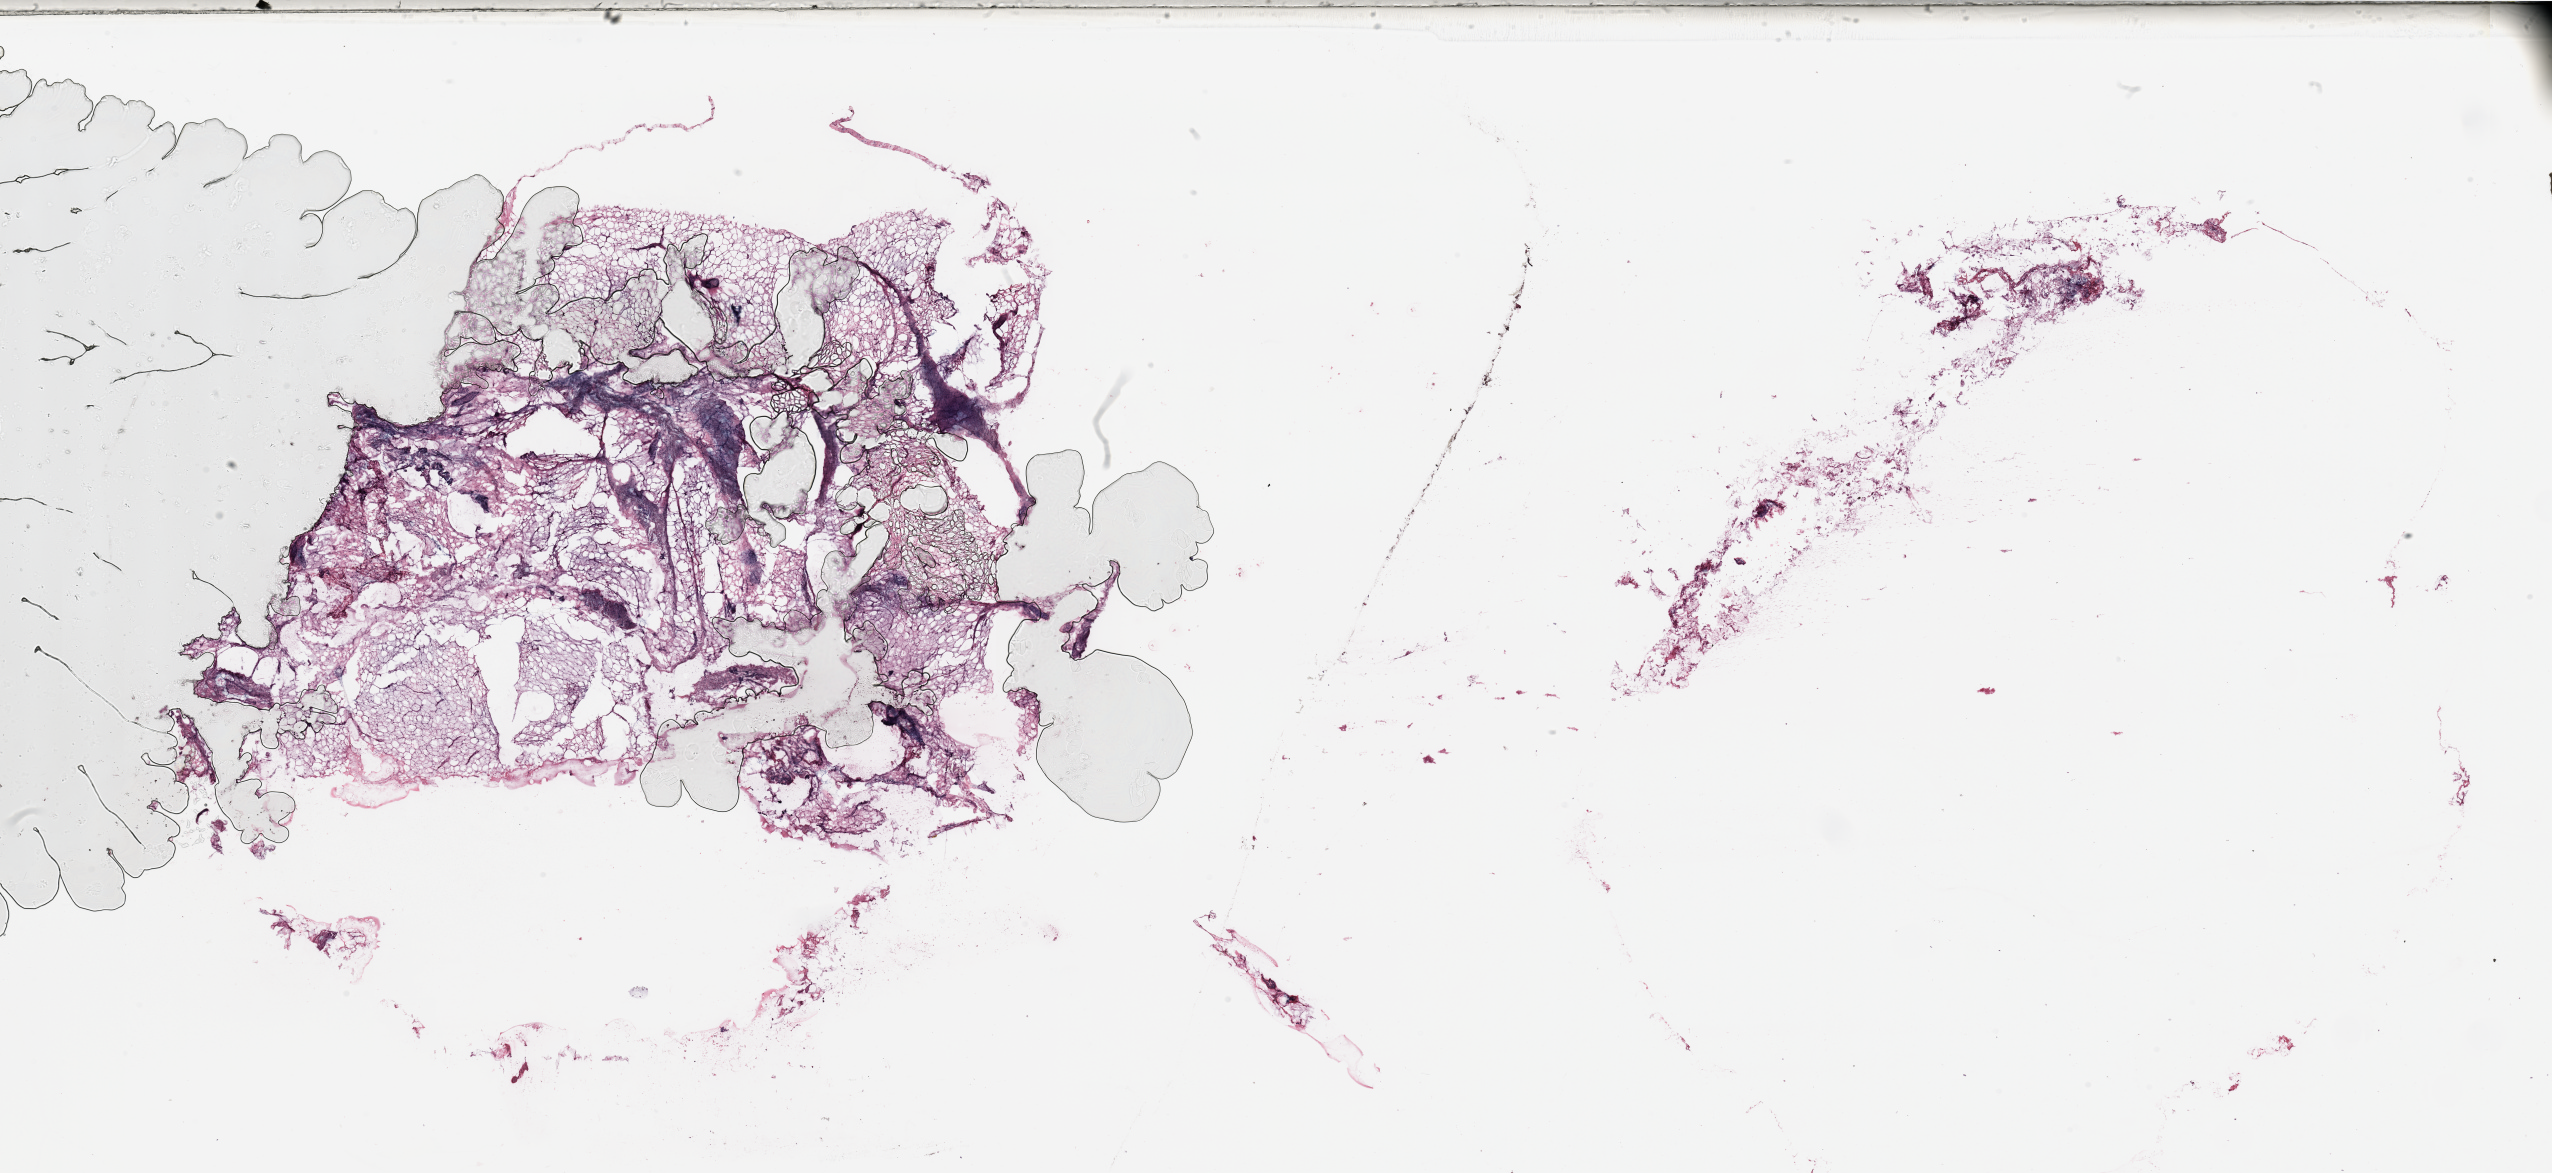
Whole-slide histology image, H&E-stained, whole scanned area (about 40.4 x 18.6 mm) shown as a low-resolution overview. Breast, tumour tissue. 64-year-old female patient.
AJCC pathologic stage: IIIA. Diagnosis: Infiltrating duct carcinoma, NOS.